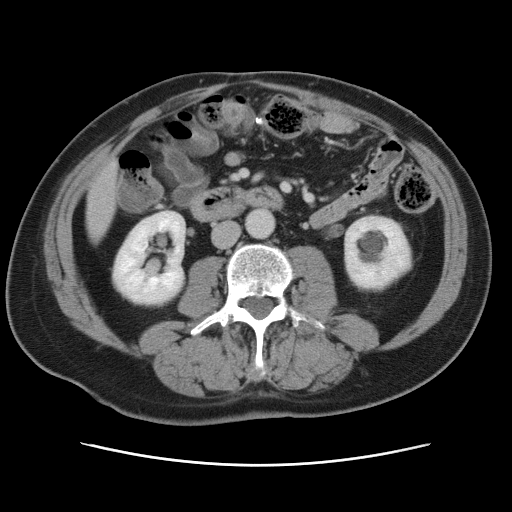
Contrast-enhanced abdominal CT, one axial slice. Slice 15 of 80 in the series (ordered by position). 120 kVp. Soft-tissue window (W 400 / L 40 HU). 5 mm slice thickness. 512 × 512 image matrix, field of view 370 × 370 mm. Male patient, age 69 years. Case-level facts recorded for this patient, not image findings: diagnosis: colorectal cancer liver metastases, imaged before liver resection; multiple liver metastases: no; largest metastasis: 5 cm; chemotherapy before resection: no.
Annotated regions visible in this slice (expert manual segmentation):
- liver: bounding box [x1, y1, x2, y2] px = [86, 163, 117, 236]
- planned liver remnant (the part of the liver to remain after resection): [91, 229, 101, 235]